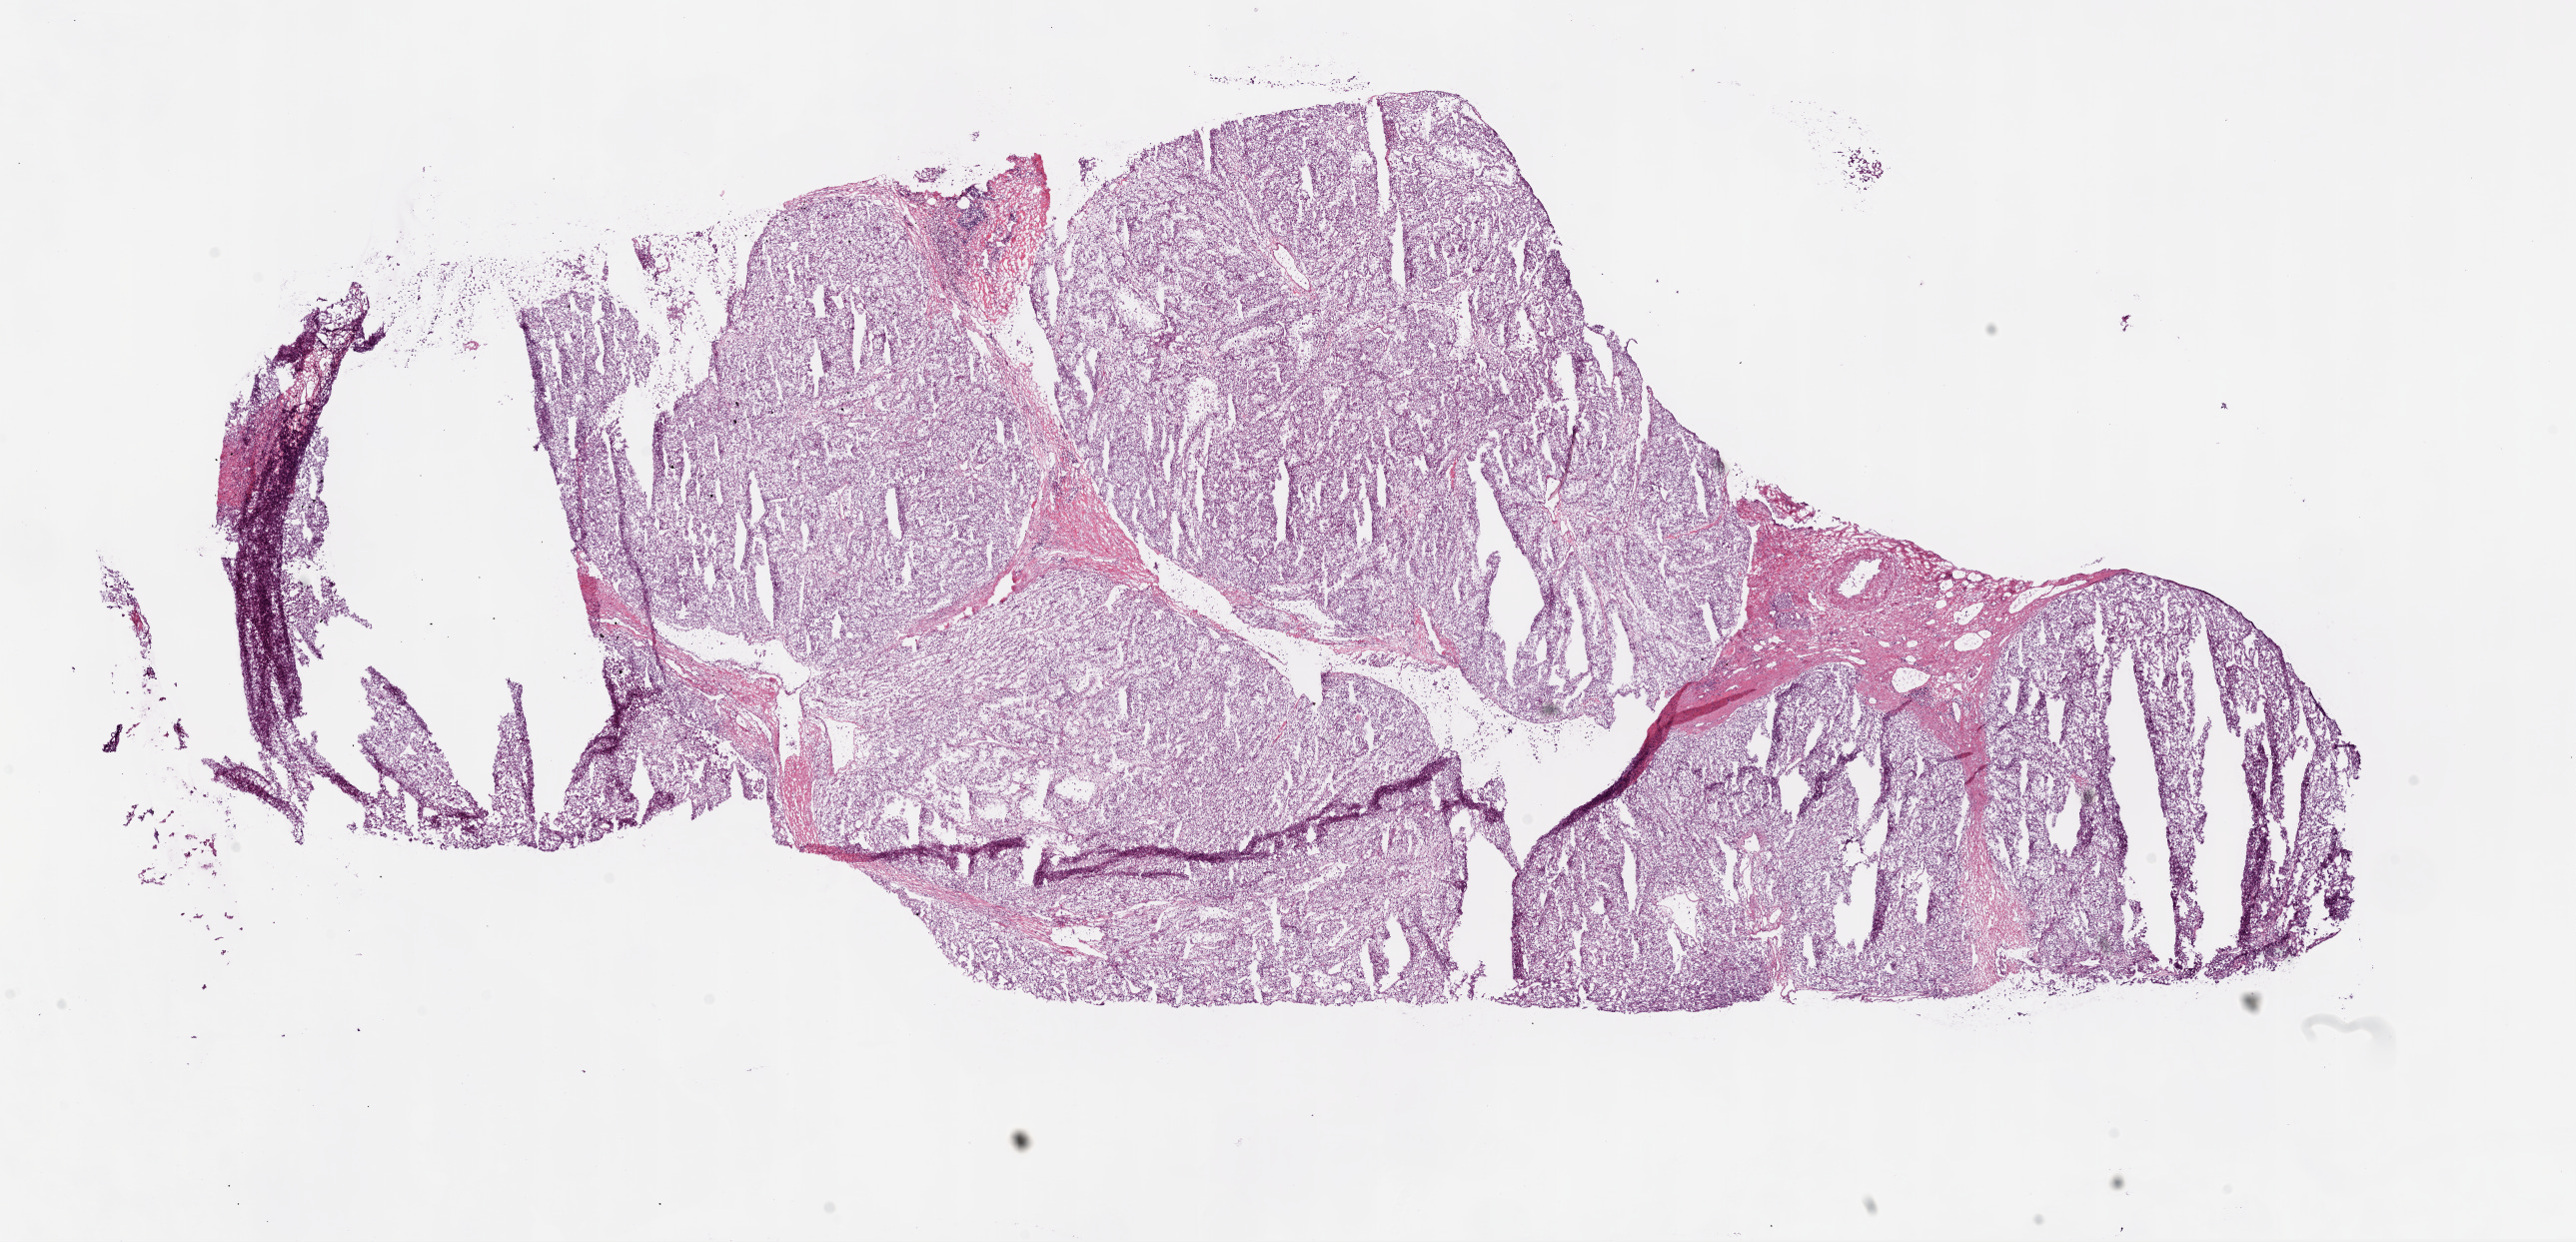
Hematoxylin and eosin (H&E) stained whole-slide image, a low-resolution overview of the entire scanned area, about 20.8 x 10.0 mm (acquisition: 20x scan), frozen section, kidney, primary tumour sample. Male patient; age at initial diagnosis 60 years. Histologic grade: G4 (undifferentiated). Slide review estimates, as recorded: tumour cells 88%, tumour nuclei 85%, normal cells 0%, stromal cells 12%, necrosis 0%.
* histologic diagnosis: Clear cell adenocarcinoma, NOS
* AJCC pathologic stage: IV (7th edition)